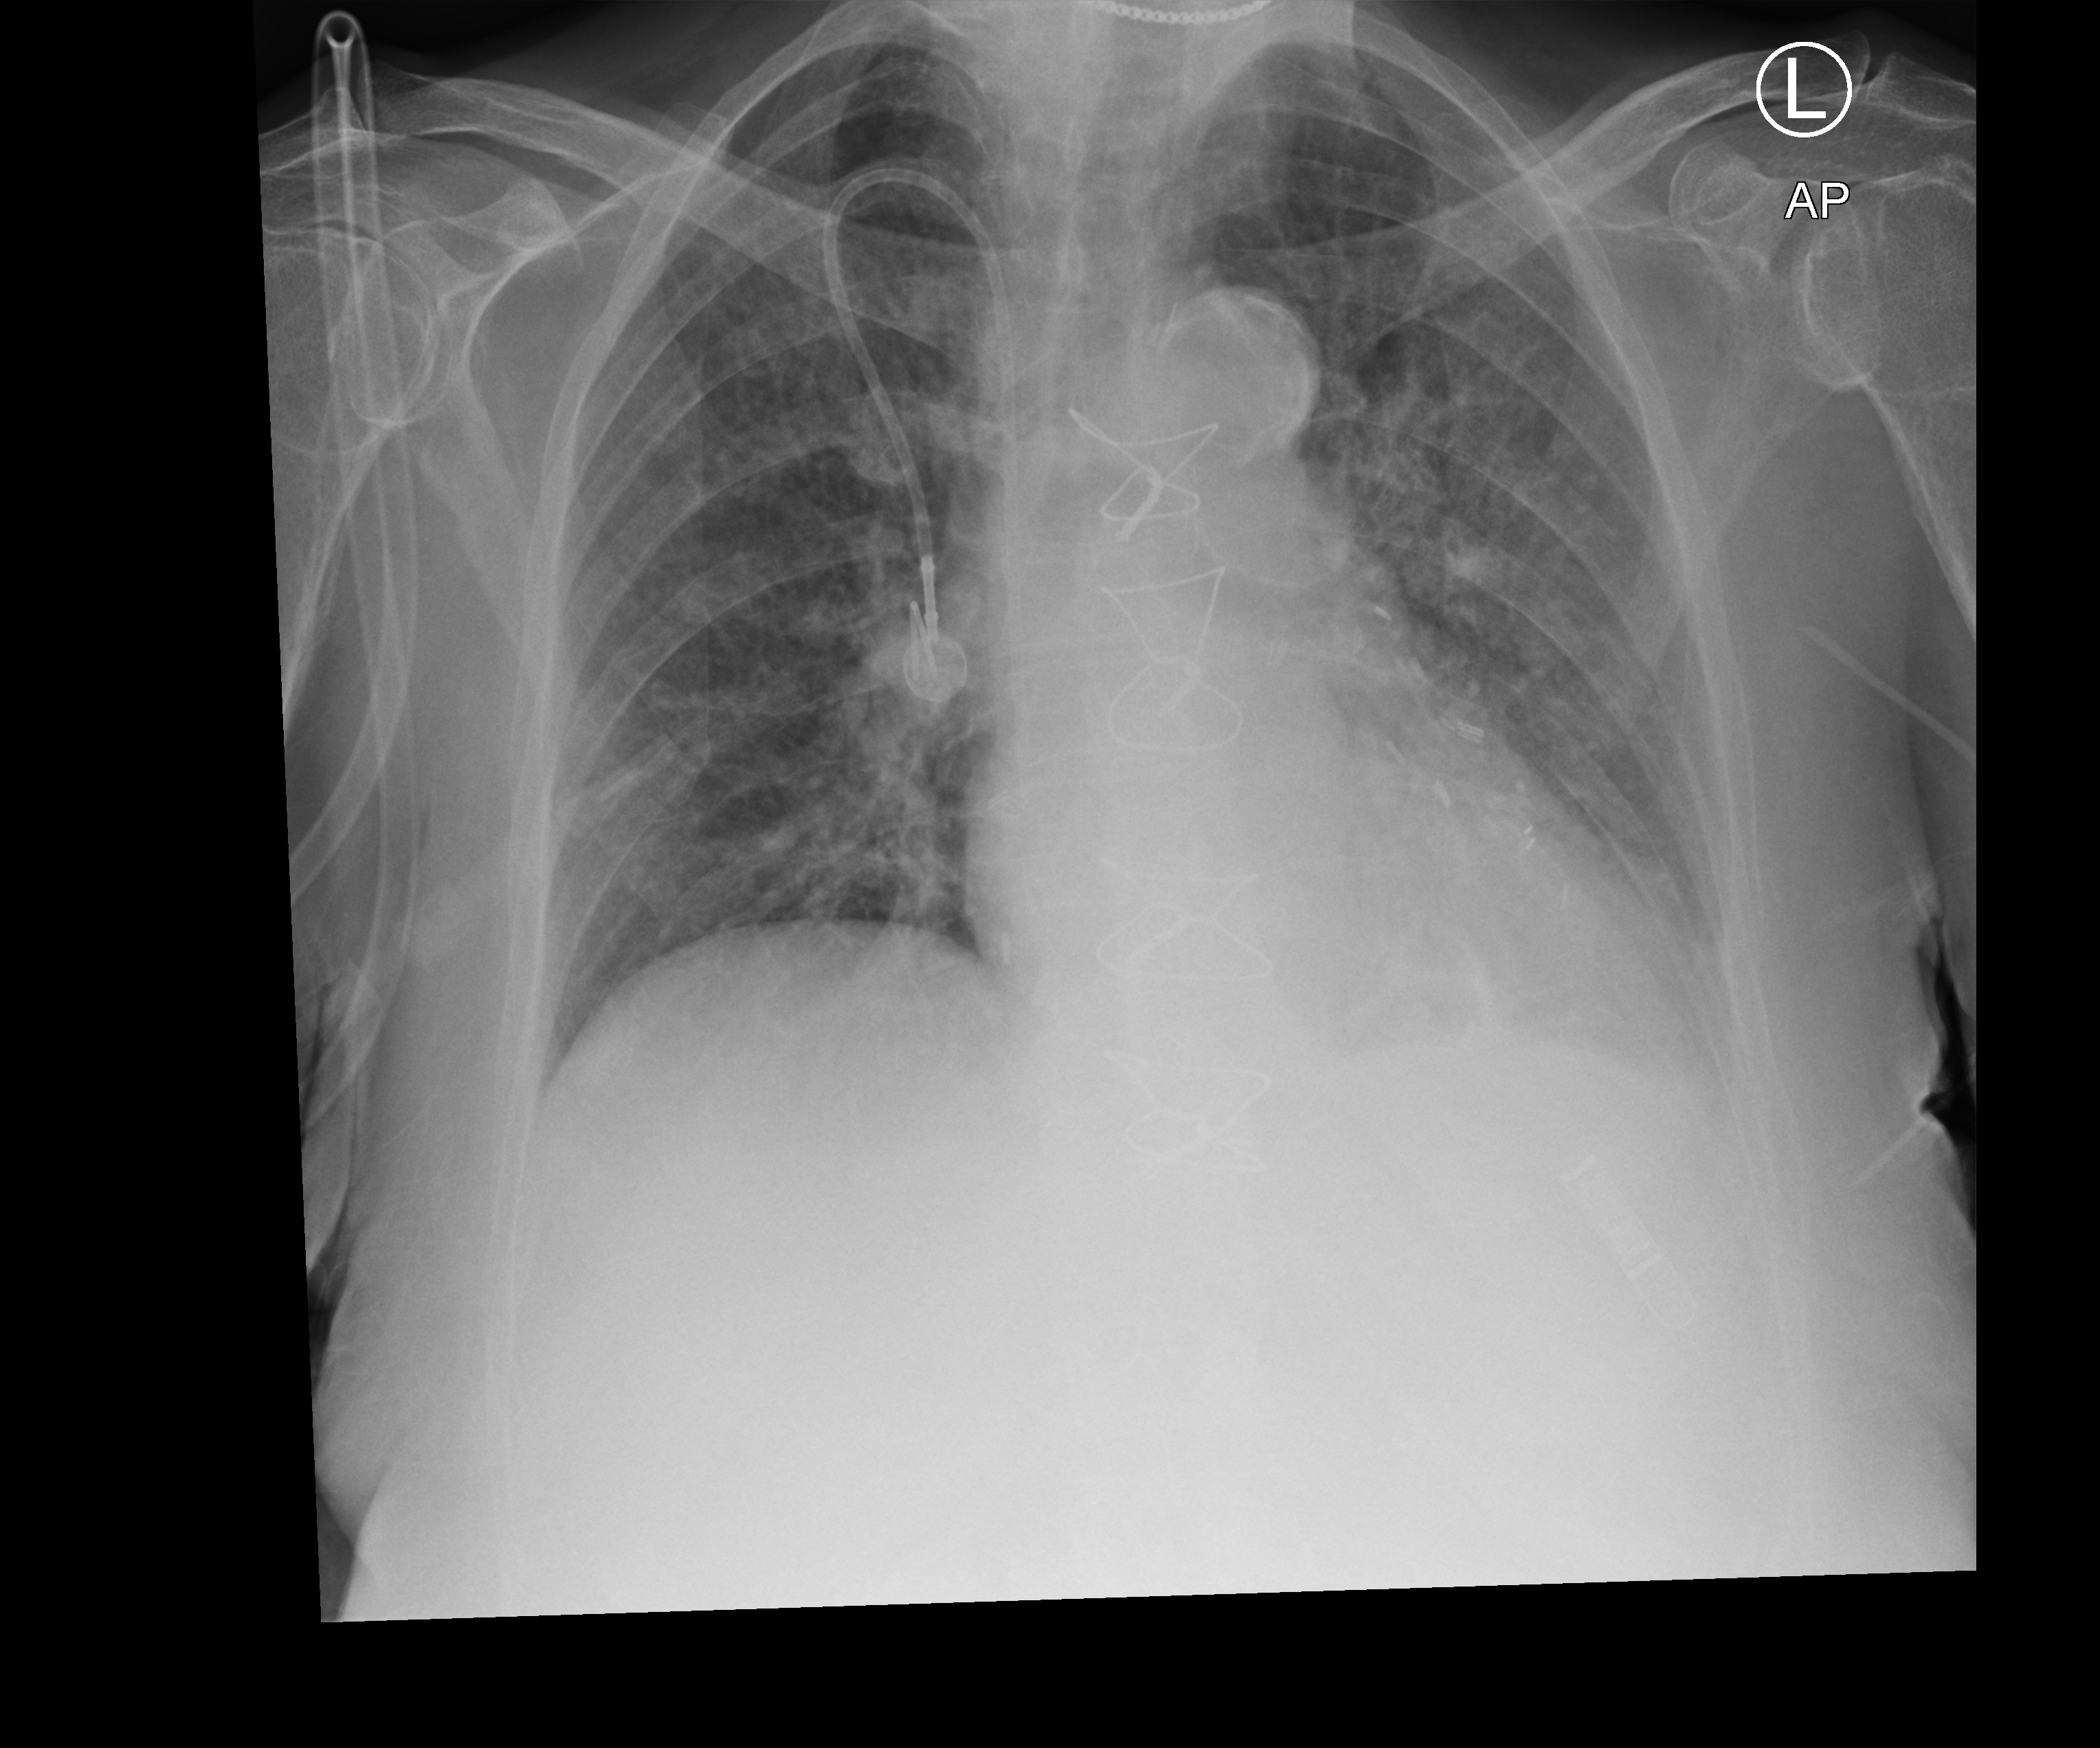
Chest radiograph; anteroposterior (AP) projection. Female patient hospitalised with COVID-19, age 75–90 years.
Admission-level facts for this patient (not findings on this image; timing relative to this image not recorded):
- other chronic lung disease (admission record): no
- mechanically ventilated during this hospital stay: no